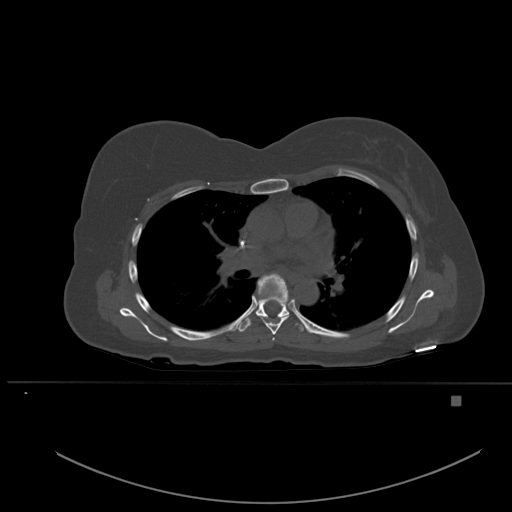
CT including the spine, one axial slice; slice 358 of 651 in the series (ordered by position); bone window (W 1800 / L 400 HU); 512 × 512 image matrix. Patient: female, 49 years. From the clinical record (not read from this slice): primary cancer: breast.
Outlined on this slice (semi-automatically segmented with operator editing):
- T4 vertebra: bounding box [x1, y1, x2, y2] px = [272, 338, 275, 341]
- T5 vertebra: [258, 273, 290, 335]
- T6 vertebra: [239, 296, 304, 332]